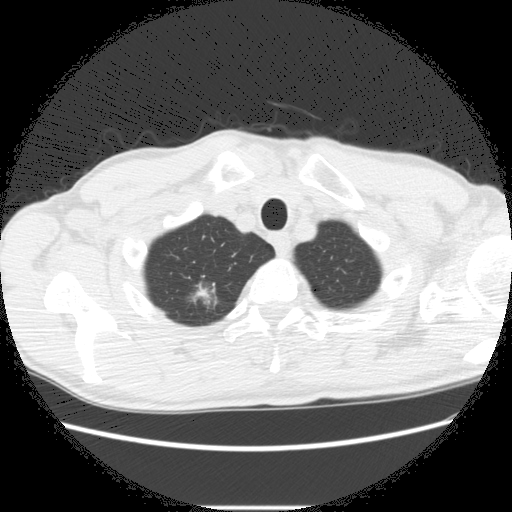
Low-dose screening chest CT, one axial slice. Position 258 of 282 along the scan axis. Reconstruction kernel STANDARD. Lung window (W 1500 / L -600 HU). 2.5 mm slice thickness. 512 × 512 image matrix, field of view 360 × 360 mm.
Outlined on this slice (outlined manually by an expert reader):
- lesion 2 (nodule, upper lobe of right lung): bounding box <190,281,213,306> (left, top, right, bottom; pixels)